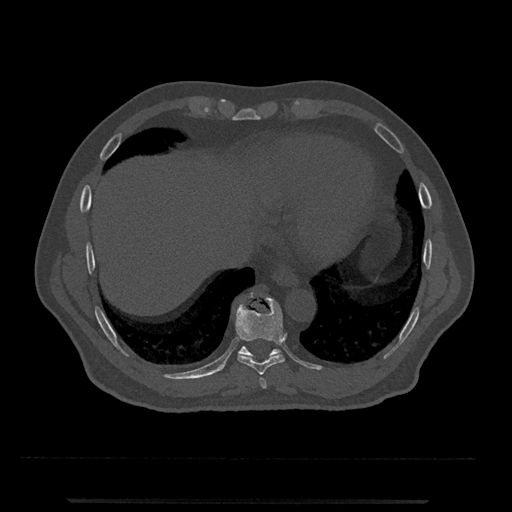
CT including the spine, one axial slice; position 557 of 797 along the scan axis; 120 kVp; bone window (W 1800 / L 400 HU); 512 × 512 image matrix, field of view 419 × 419 mm. Male patient, age 63 years. From the clinical record (not read from this slice): primary cancer: prostate.
Structures marked on this image (semi-automatic segmentation, software-assisted and operator-edited):
- T10 vertebra: bounding box <238,346,281,358> (left, top, right, bottom; pixels)
- T8 vertebra: <259,377,267,389>
- T9 vertebra: <235,293,285,375>